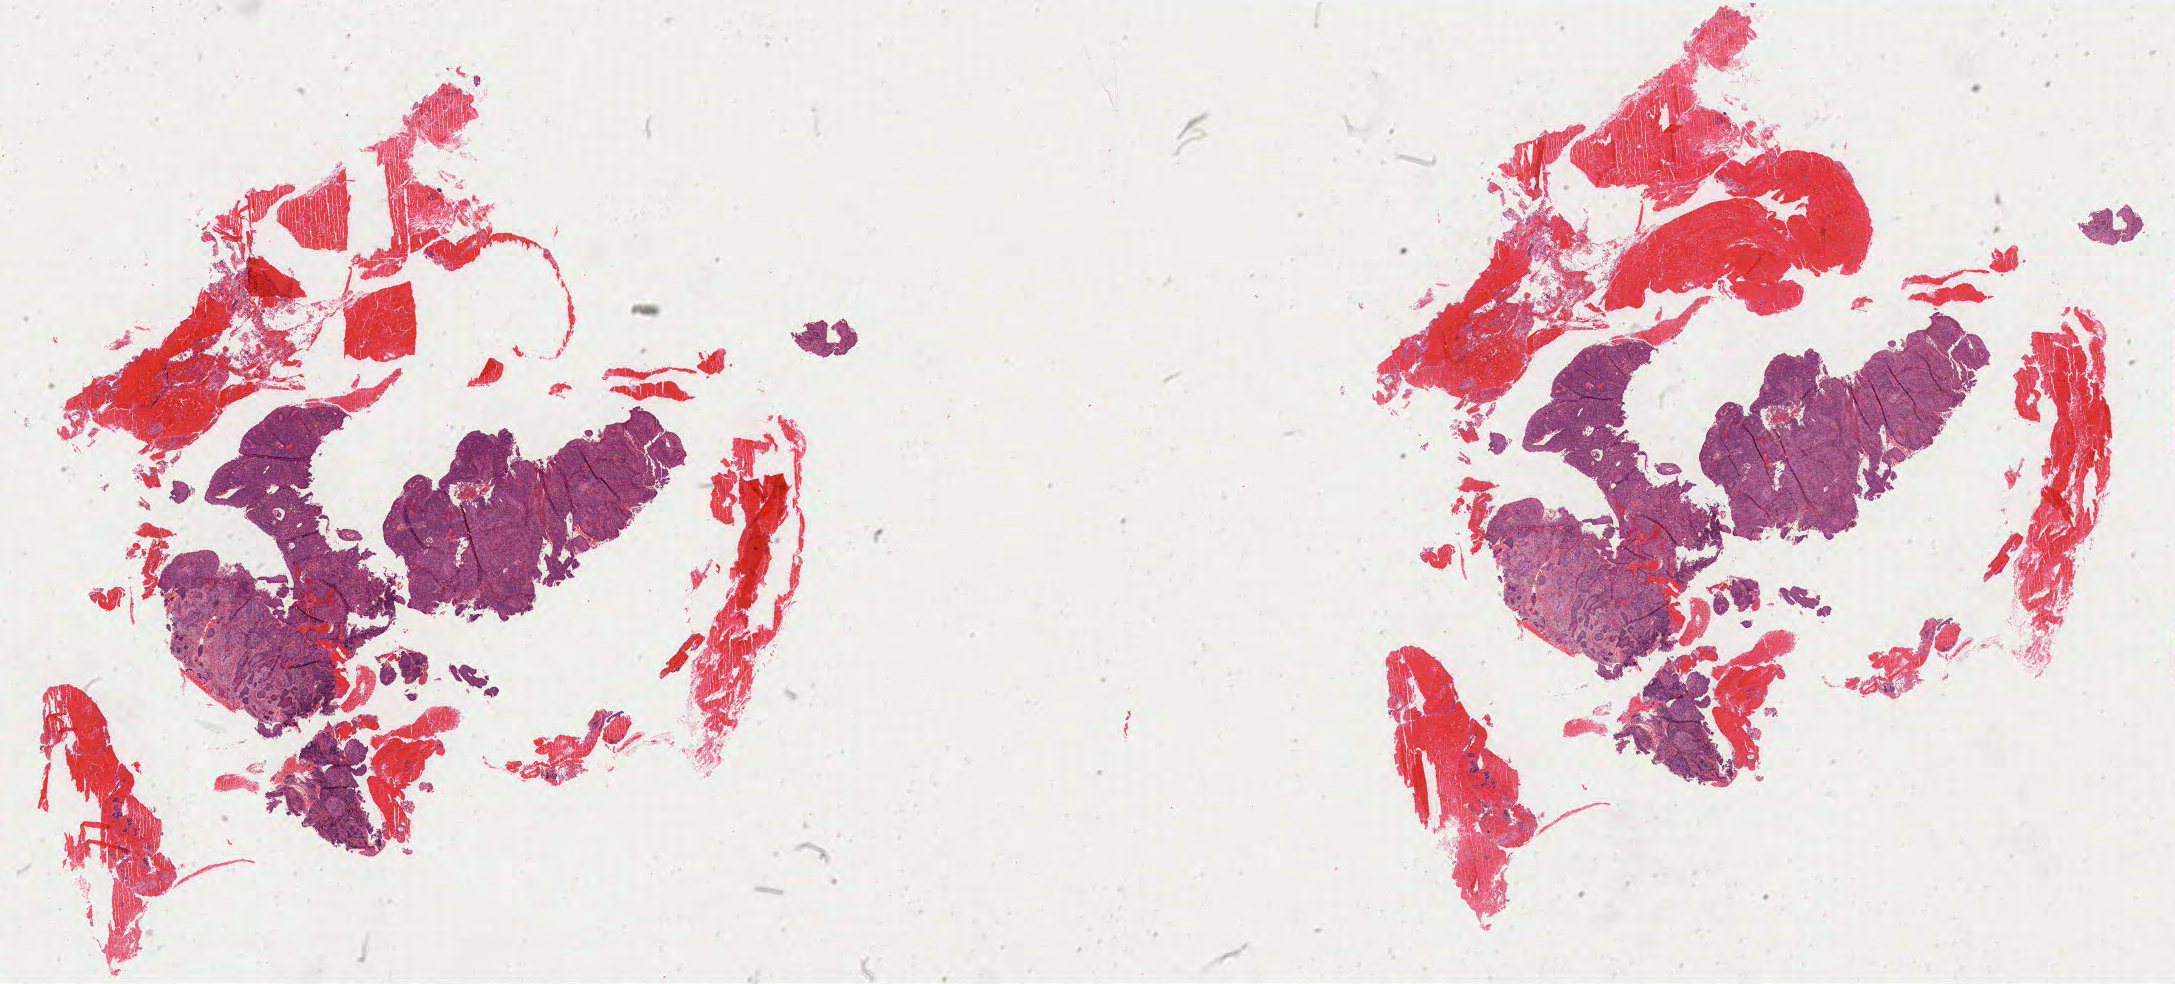
Digitized H&E-stained tissue section (whole slide), low-resolution overview of the scanned area, about 34.8 x 15.8 mm. FFPE section. Cervix, primary tumour sample. Patient: female, age at initial diagnosis 69 years. Histologic grade: G3 (poorly differentiated).
Histologic diagnosis: Squamous cell carcinoma, NOS (cervix uteri). FIGO stage: IB2. Lymph nodes positive (case pathology): 0 of 10 examined.